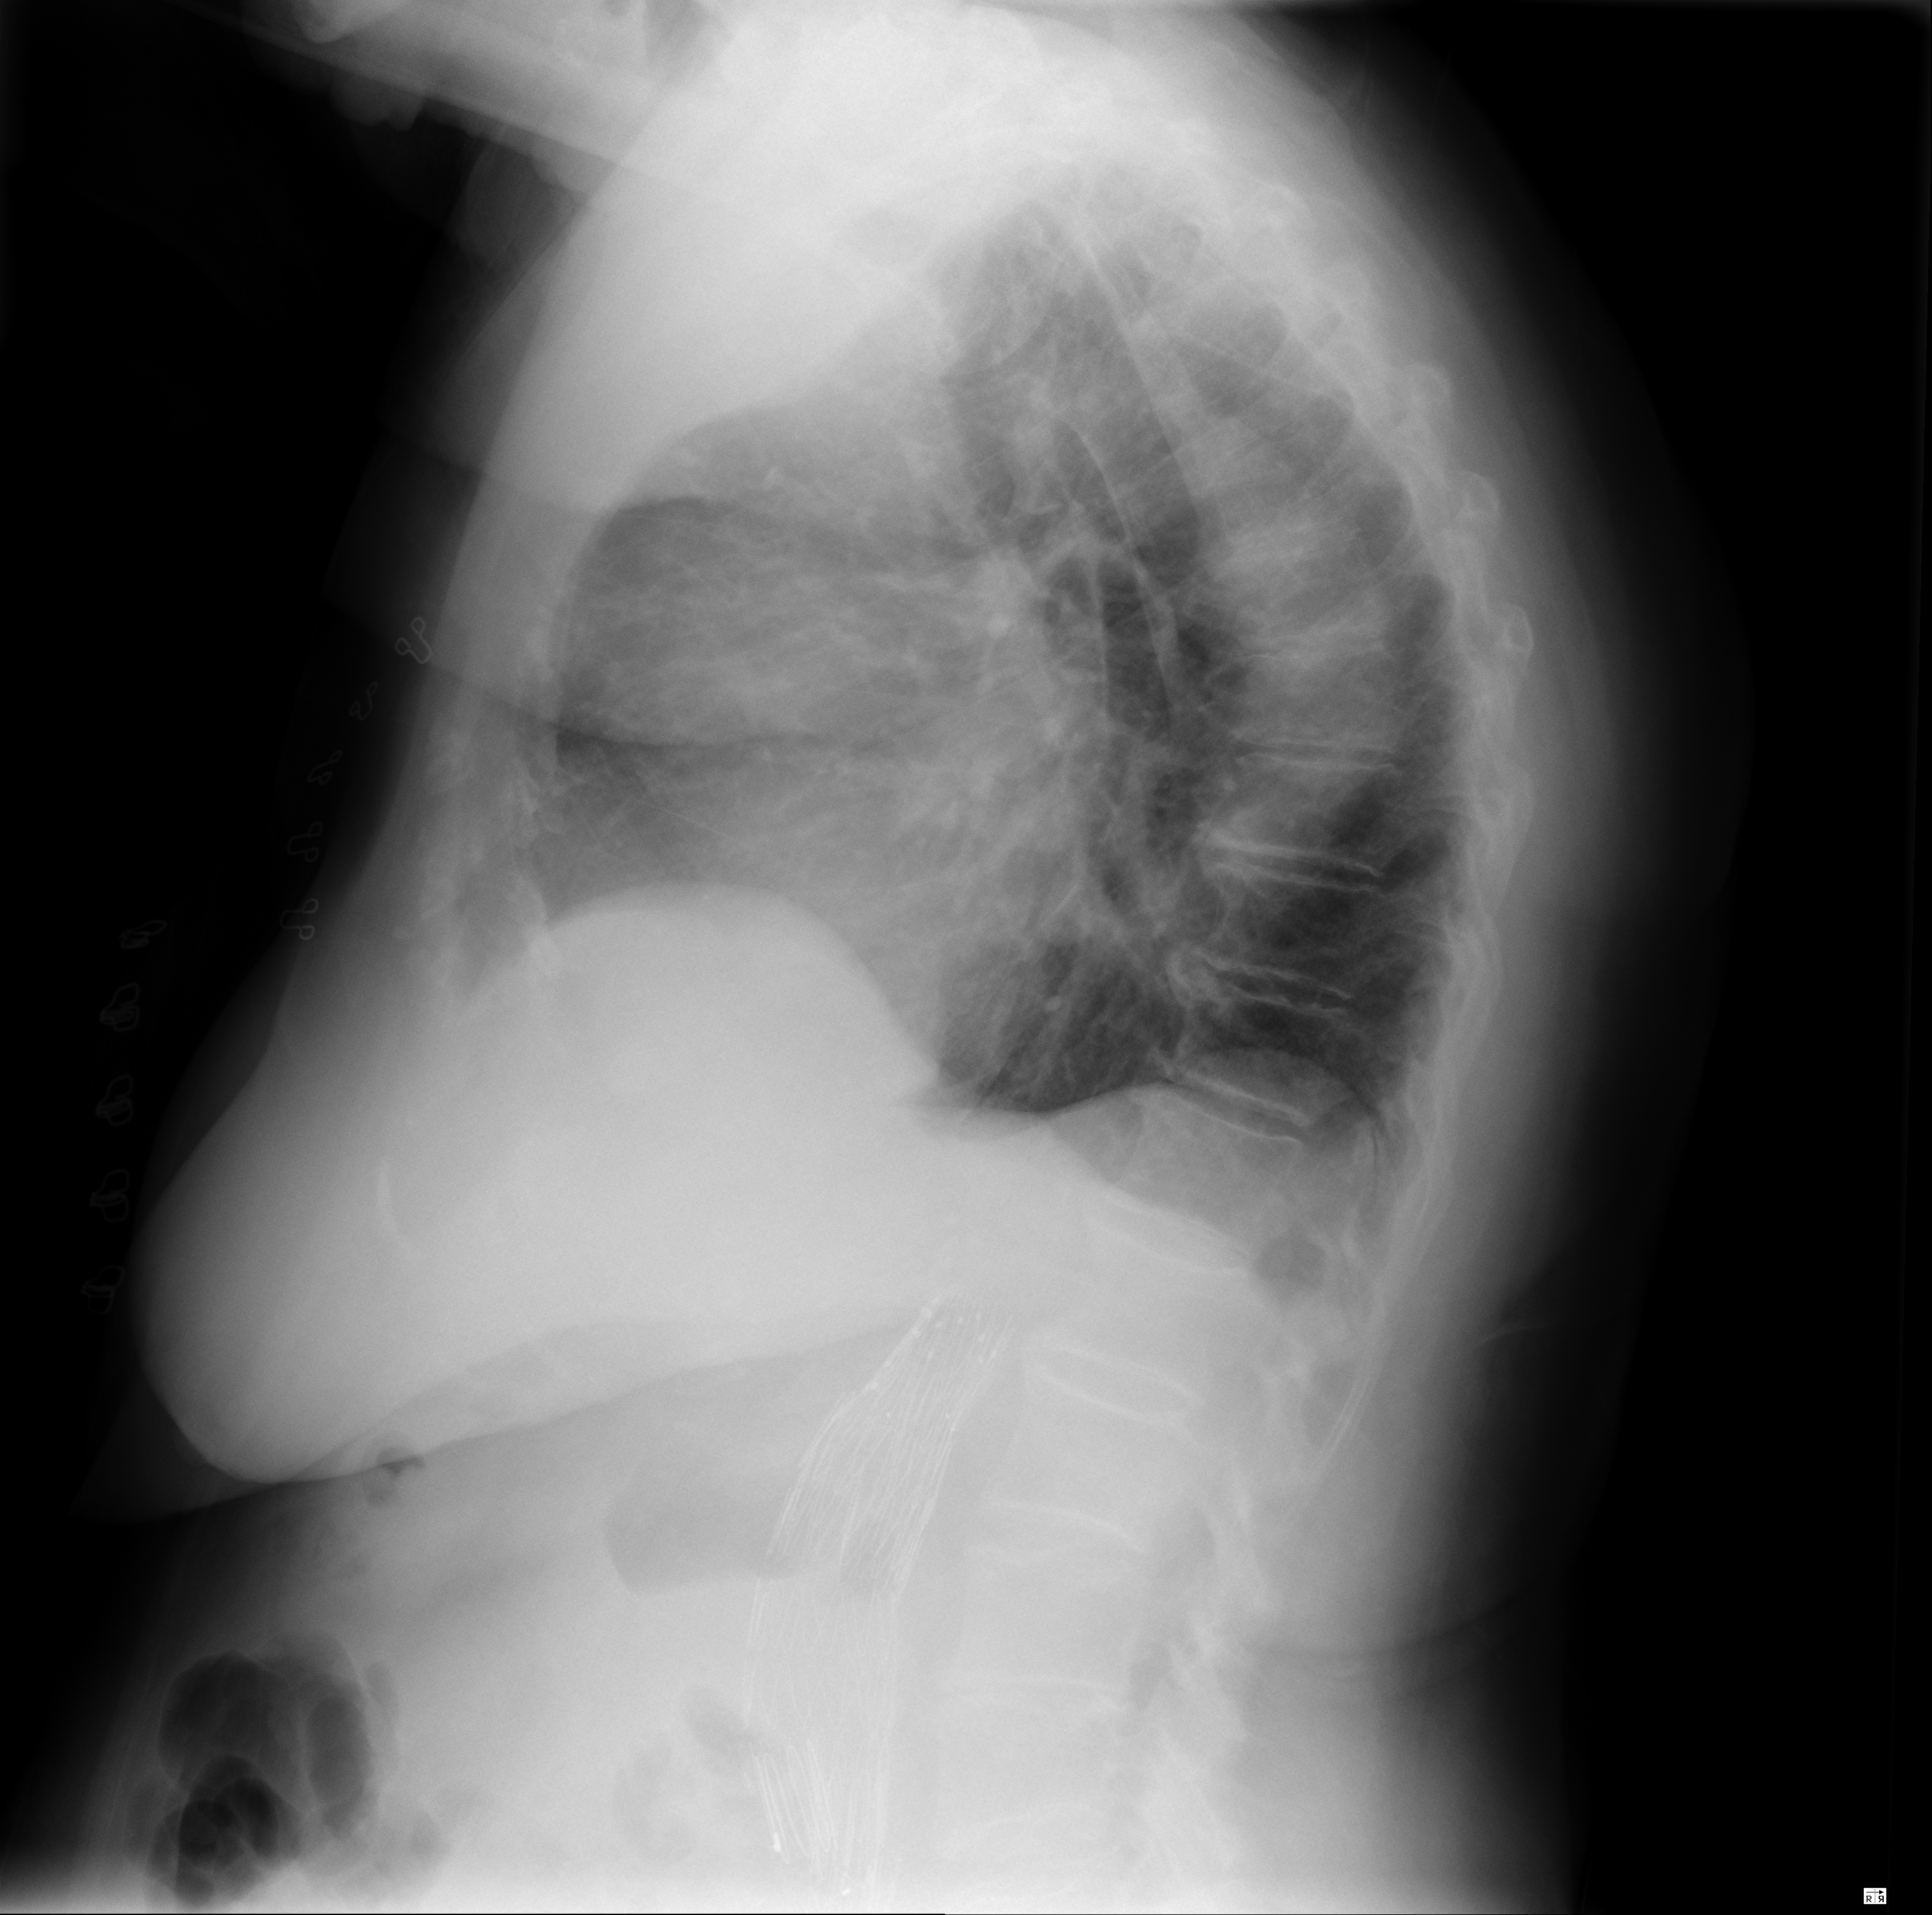
Chest radiograph, lateral projection. Female patient, age 88 years; imaged 0 days after the COVID-19 diagnosis.
Radiologist key findings (as recorded): No pleural effusions.